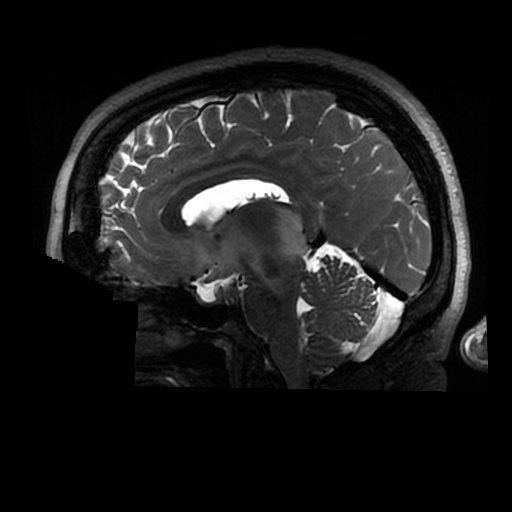
Brain MRI from a brain-tumour surgery series, one sagittal slice. Slice 159 of 320 in the series (ordered by position). 0.6 mm slice thickness. 512 × 512 image matrix, field of view 240 × 240 mm. Case-level facts recorded for this patient, not image findings: histopathology: Astrocytoma; WHO grade: 2; IDH mutation: yes.
Structures marked on this image (manually delineated by an expert):
- tumour: box from (x=274, y=206) to (x=305, y=262) px